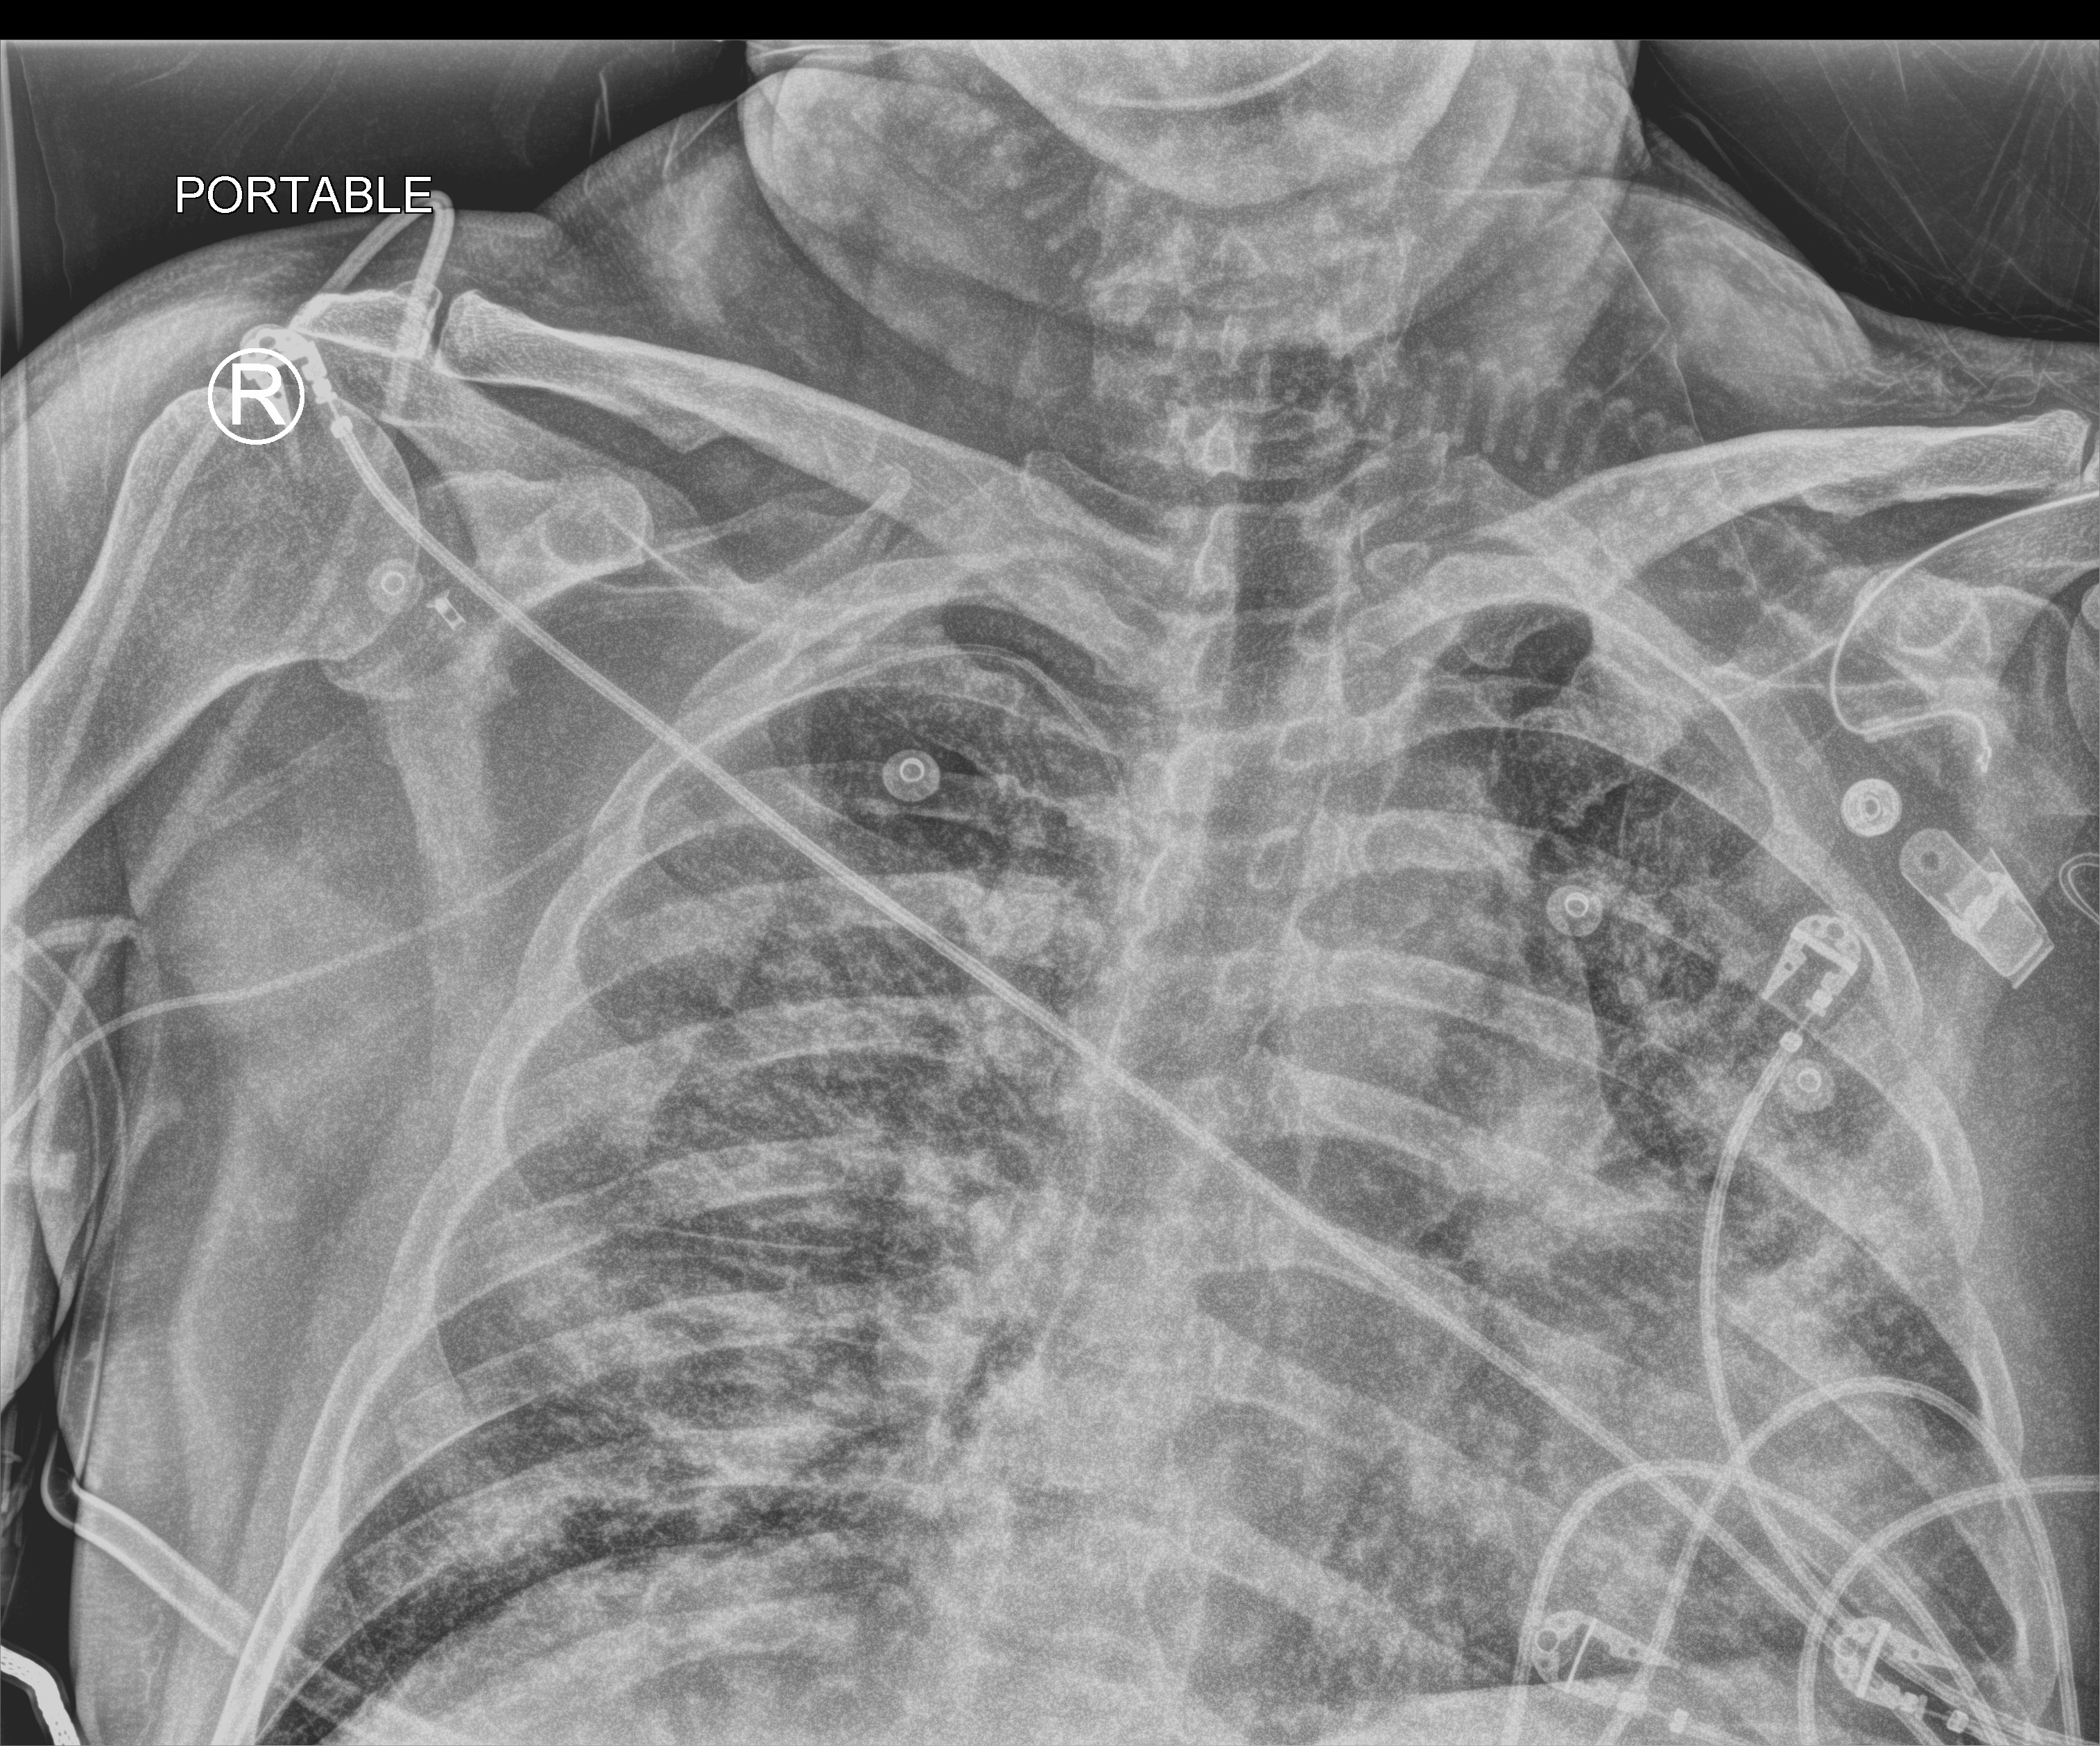
Bedside chest radiograph (computed radiography); anteroposterior (AP) projection. Male patient hospitalised with COVID-19, age 18–59 years.
From the hospital-stay record, not from the radiograph (when in the stay this image was taken is not recorded):
- mechanically ventilated during this hospital stay: yes